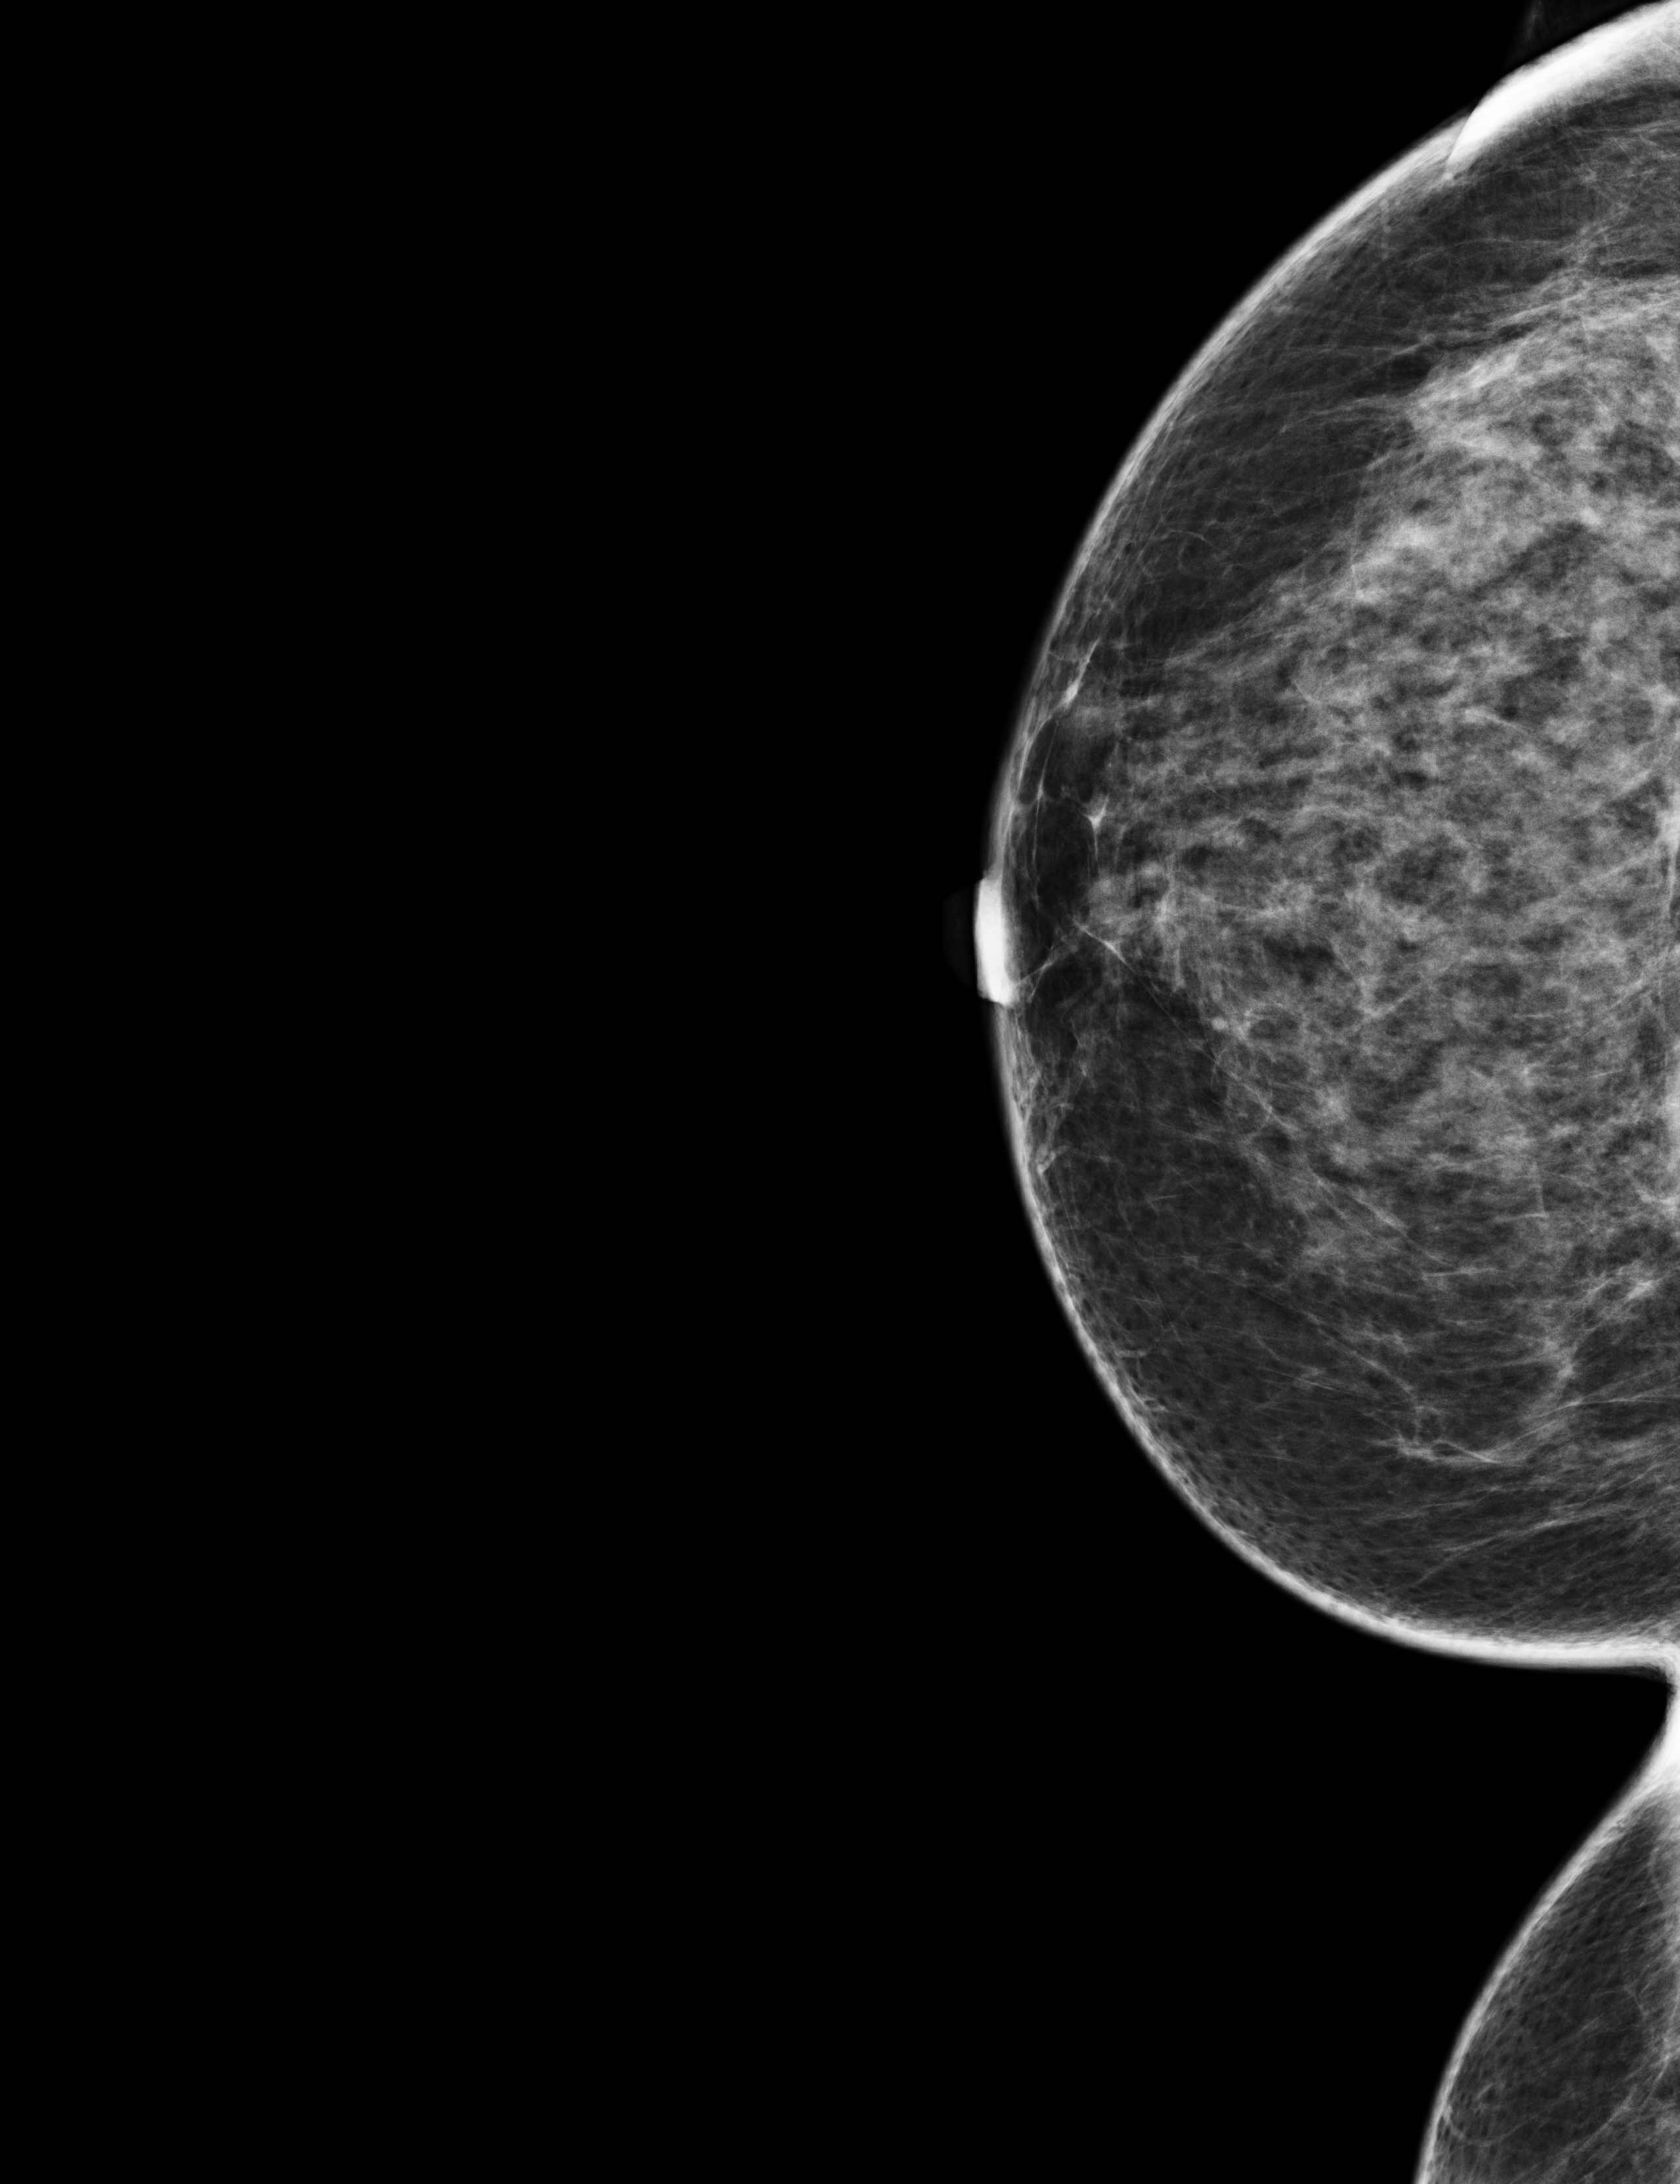
Screening examination, compressed breast thickness 74 mm, system: Selenia Dimensions. Female patient, age 53 years.
Image type: full-field digital mammogram. Breast: right. Projection: craniocaudal (CC) view.